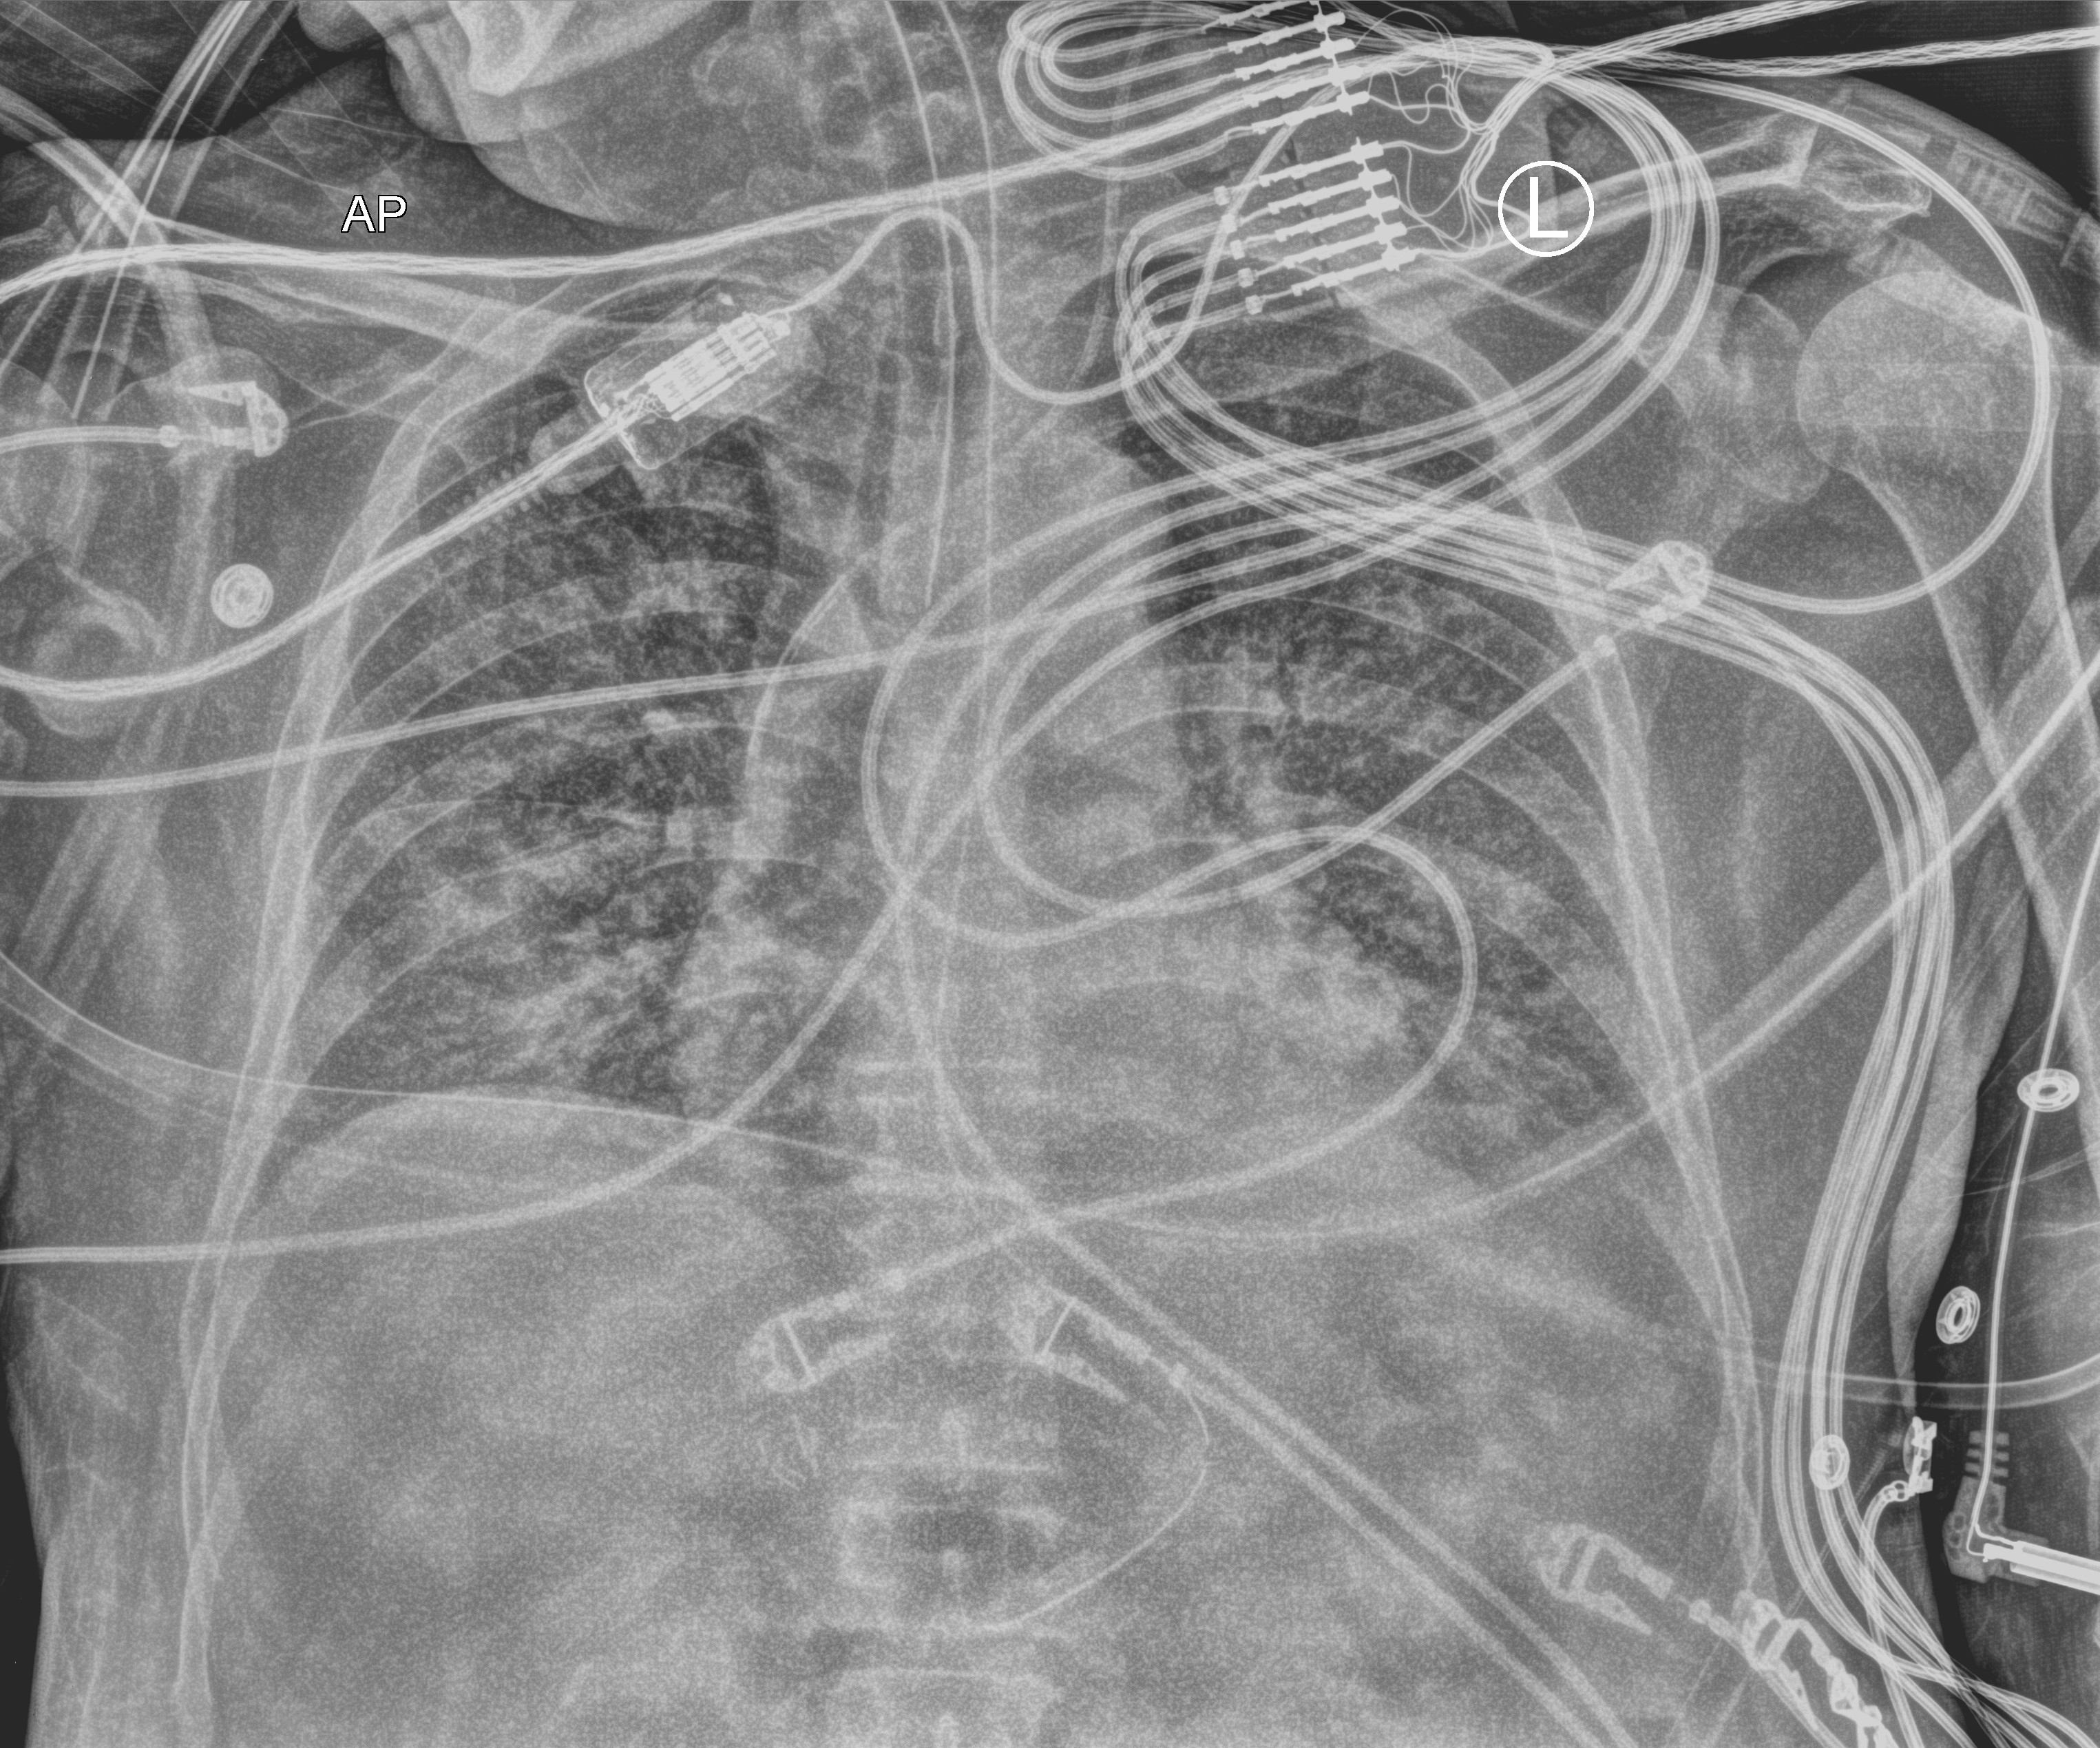
Chest X-ray (portable); anteroposterior (AP) projection. Male patient hospitalised with COVID-19, age 60–74 years.
From the hospital-stay record, not from the radiograph (when in the stay this image was taken is not recorded):
- length of hospital stay: 23 days
- admitted to intensive care during this hospital stay: yes
- hypertension (admission record): no